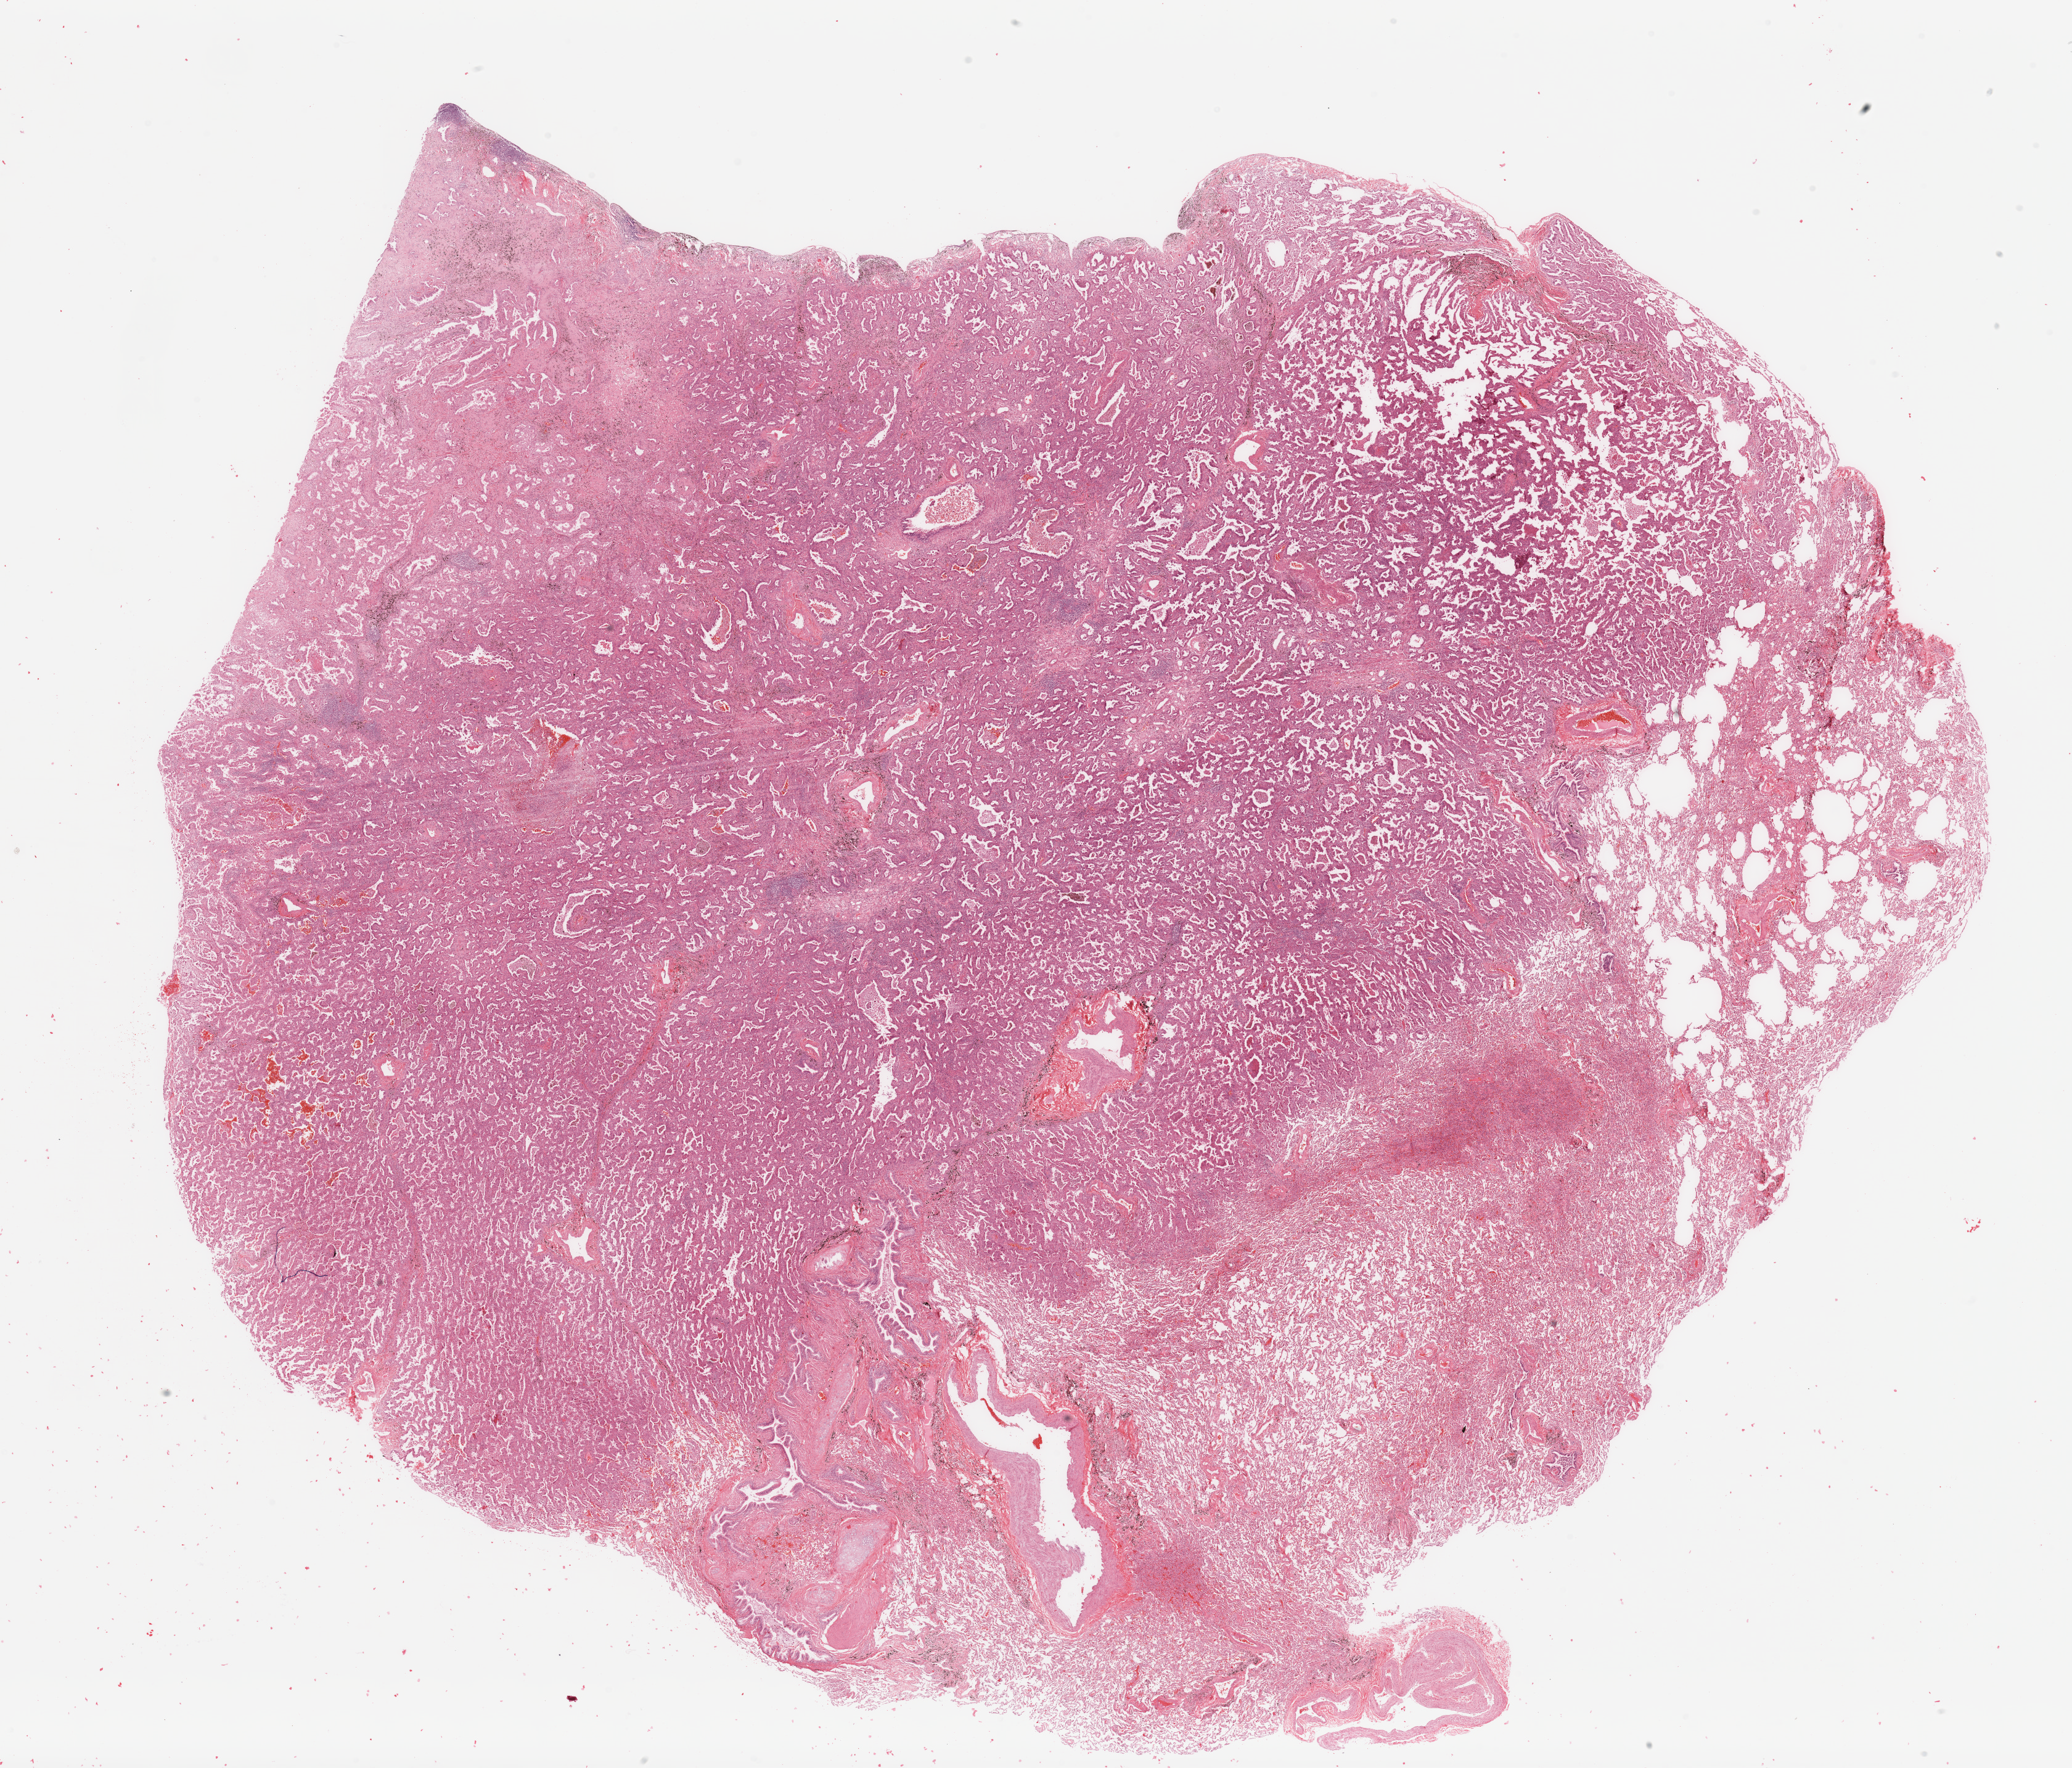
Whole-slide histology image, H&E-stained — a low-resolution overview of the entire scanned area, about 26.6 x 22.7 mm (acquisition: 20x scan); tumour tissue sample, lung. 64-year-old male patient. Histologic grade: G2 (moderately differentiated).
* histologic diagnosis: Adenocarcinoma, NOS
* primary tumour site (as recorded): right lower lobe
* AJCC pathologic stage: IIA